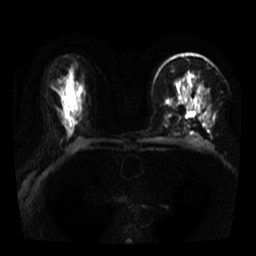
Breast MRI, one axial slice; slice 22 of 39 in the series (ordered by position); diffusion-weighted series; image 2 of 4 stored at this slice position (different b-values; order by instance number); 3 T; 256 × 256 image matrix, field of view 320 × 320 mm. Female patient.
Structures marked on this image (outlined manually by an expert reader):
- tumour on diffusion-weighted imaging: bounding box <185,106,189,114> (left, top, right, bottom; pixels)